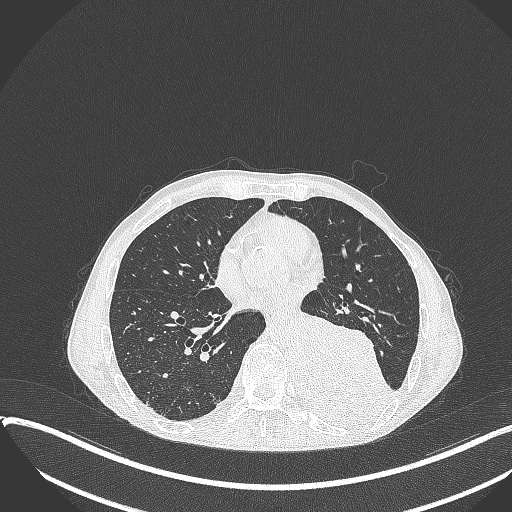
Chest CT, one axial slice. Position 154 of 401 along the scan axis. 120 kVp. Lung window (W 1500 / L -600 HU). 1 mm slice thickness. 512 × 512 image matrix, field of view 400 × 400 mm. Patient: male, 57 years. From the clinical record (not read from this slice): clinical TNM (as recorded): T4 N0 M0.
Annotated regions visible in this slice (rectangle marked by the reading radiologist):
- lung tumour (recorded histology: squamous cell carcinoma): bounding box [x1, y1, x2, y2] px = [290, 306, 390, 434]